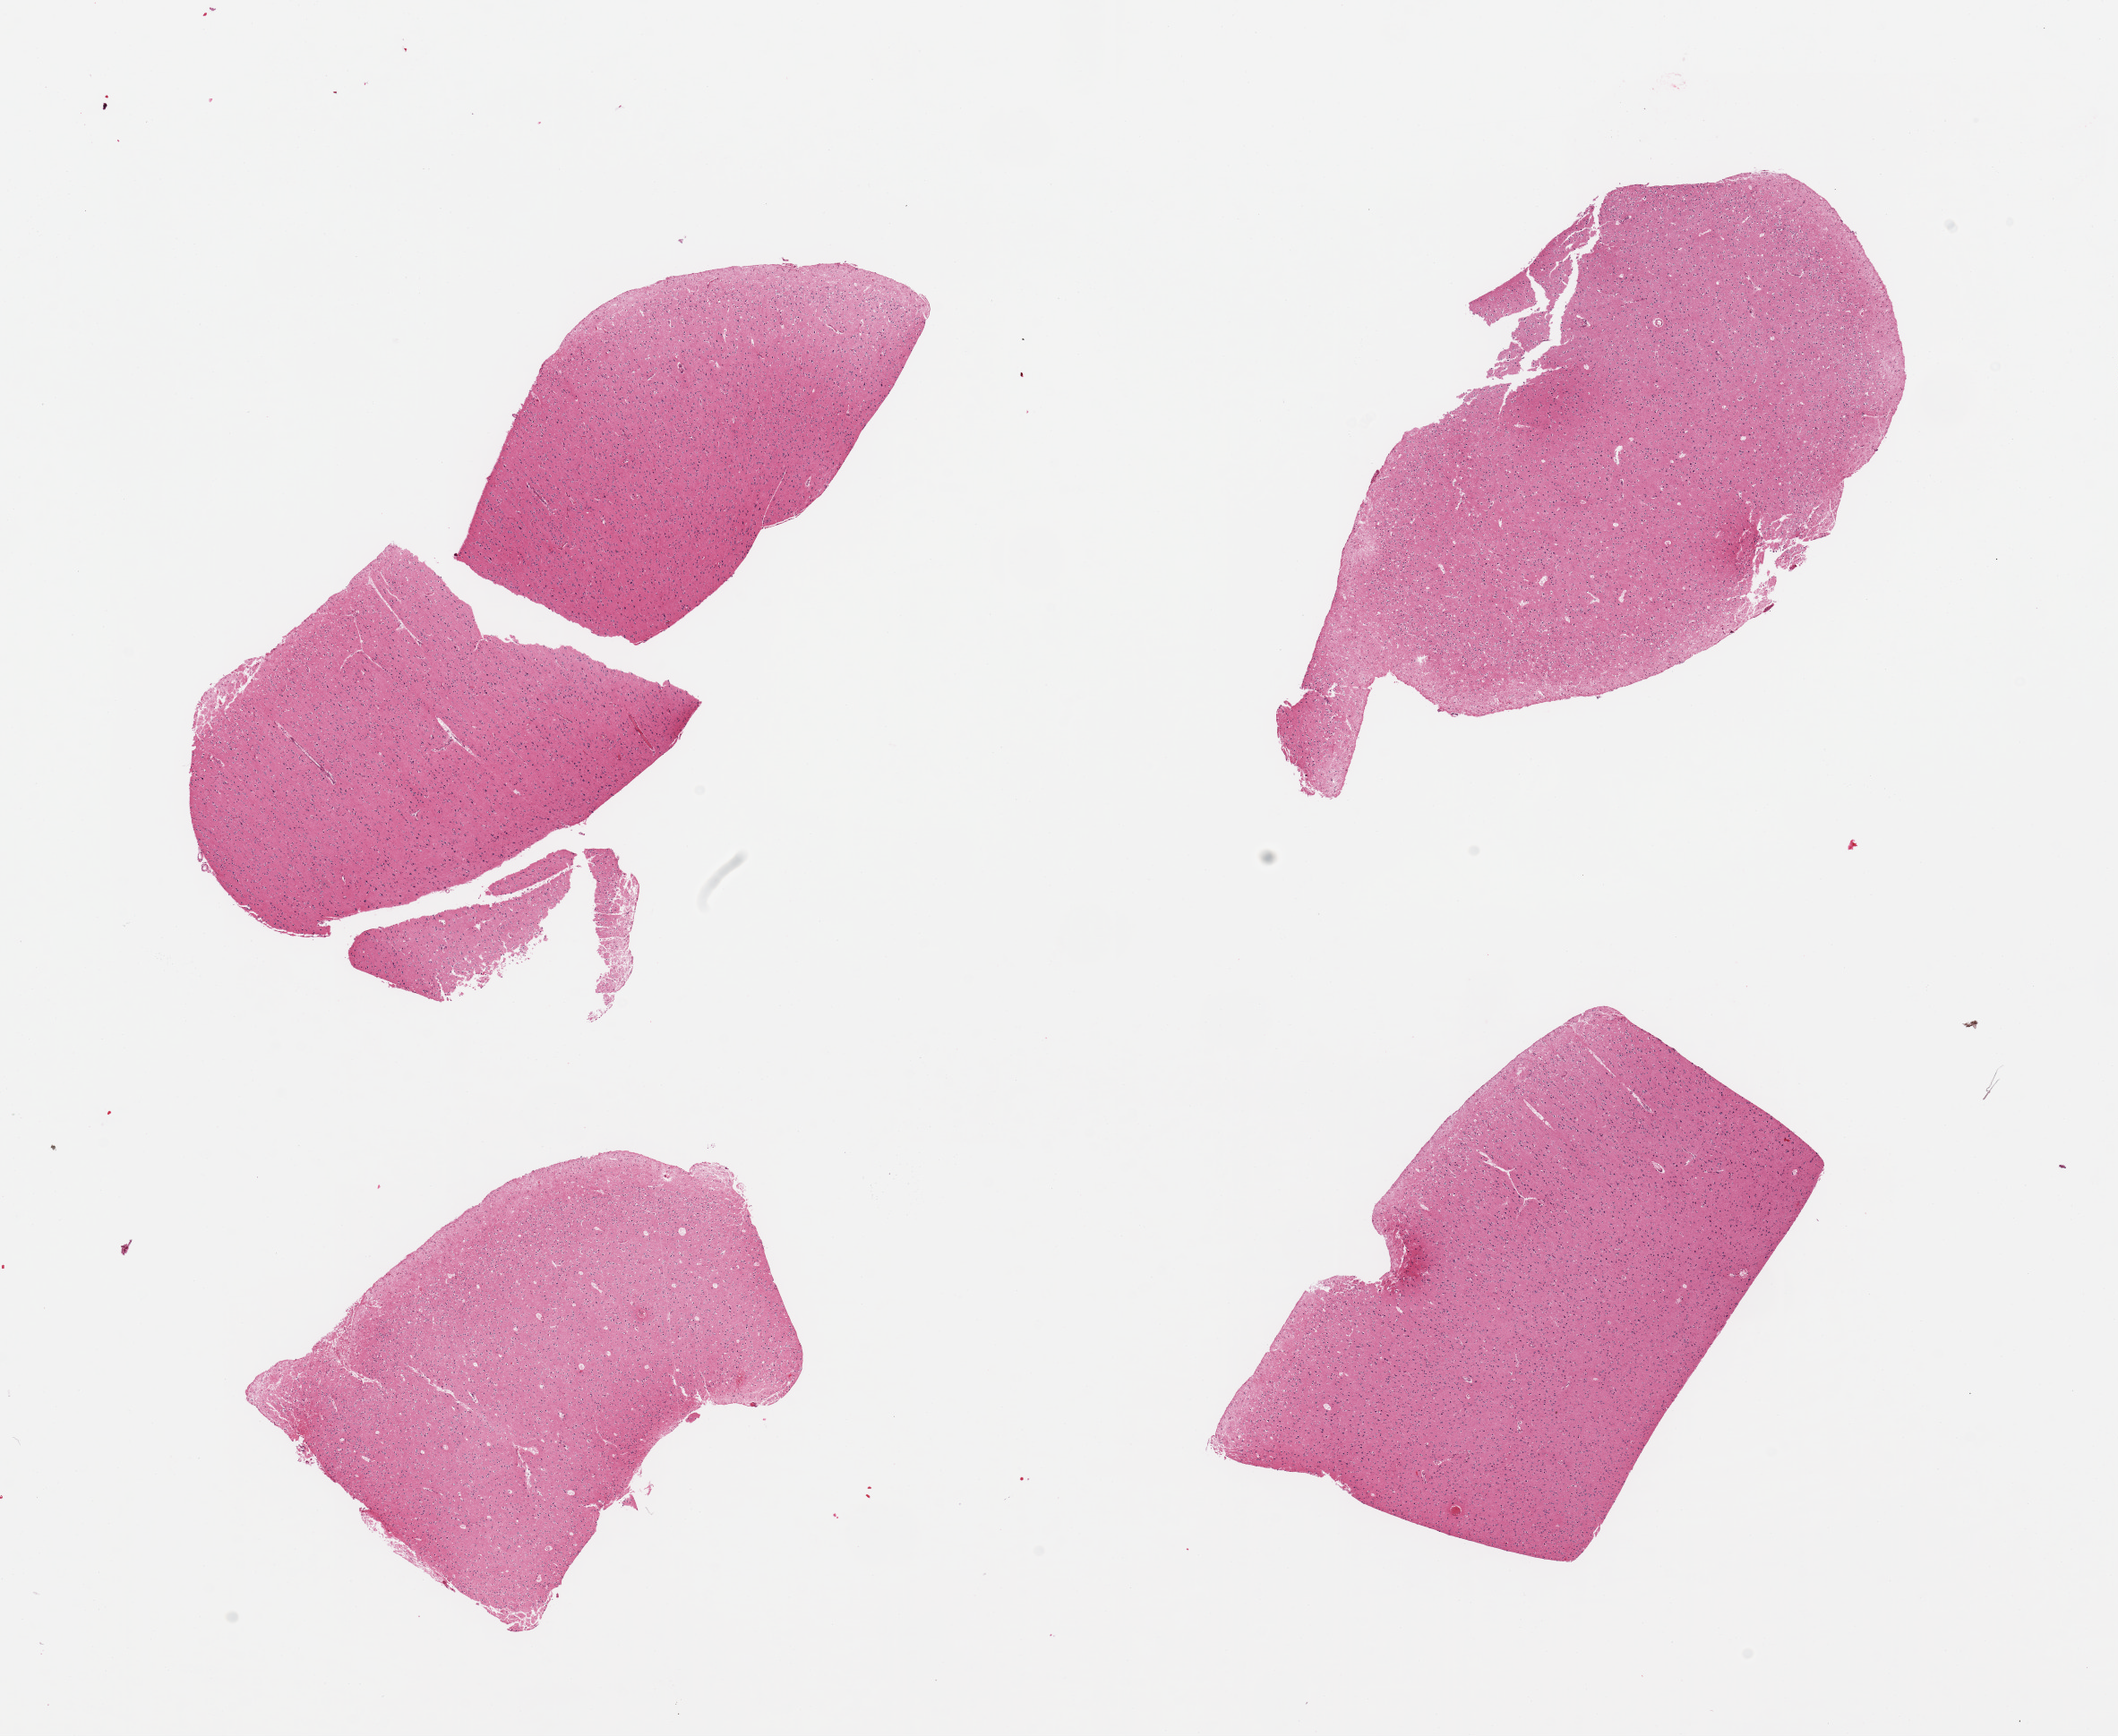
Digitized haematoxylin and eosin-stained section, a low-resolution overview of the entire scanned area, about 18.7 x 15.3 mm, PAXgene-fixed, paraffin-embedded tissue, target tissue: cerebral cortex, tissue donor sample. Male donor.
- reviewer comment on this tissue sample: 4 pieces